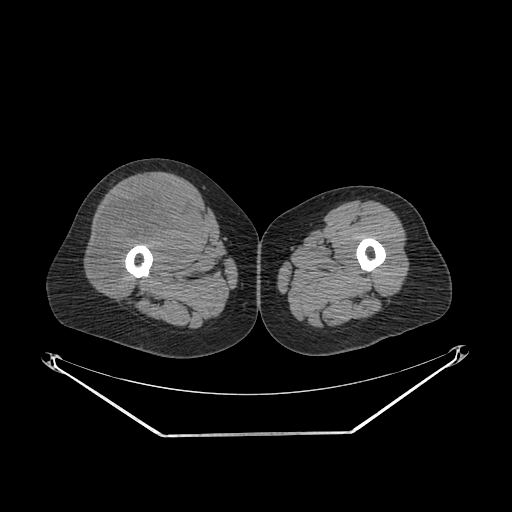
CT of an extremity soft-tissue mass (from a PET/CT study), one axial slice; position 247 of 311 along the scan axis; reconstruction kernel SOFT; soft-tissue window (W 400 / L 40 HU); 3.75 mm slice thickness; 512 × 512 image matrix, field of view 500 × 500 mm. Female patient. From the clinical record (not read from this slice): histological type: pleiomorphic undifferentiated sarcoma; grade: high; site of the primary tumour: right quadricep.
Structures marked on this image (expert contour drawn on MRI and transferred to this co-registered scan by the dataset authors):
- tumour plus oedema (research contour): bounding box <94,185,197,286> (left, top, right, bottom; pixels)
- tumour (research contour): <94,185,197,286>